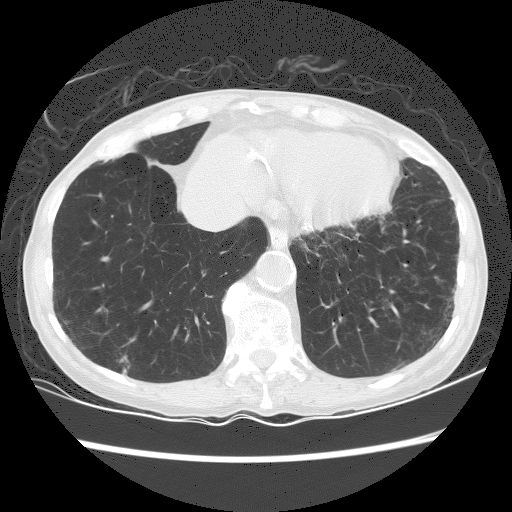
Low-dose screening chest CT, one axial slice. Position 53 of 156 along the scan axis. Reconstruction kernel BONE. 120 kVp. Lung window (W 1500 / L -600 HU). 512 × 512 image matrix.
Structures marked on this image (expert manual segmentation):
- lesion 1 (tumor, lower lobe of right lung): box from (x=120, y=356) to (x=129, y=374) px